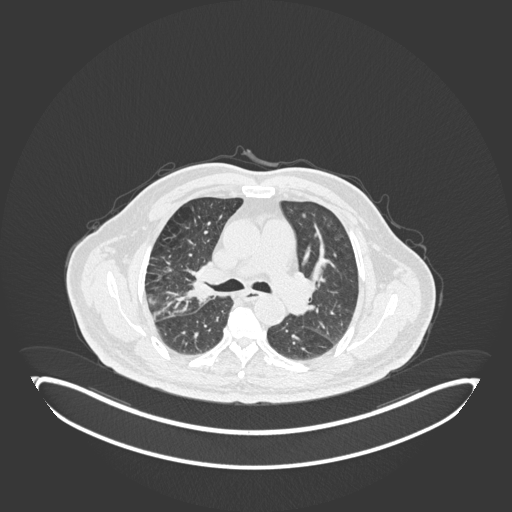
Chest CT, one axial slice. Slice 109 of 247 in the series (ordered by position). 120 kVp. Lung window (W 1500 / L -600 HU). 1 mm slice thickness. 512 × 512 image matrix, field of view 500 × 500 mm. Male patient, age 72 years. Case-level facts recorded for this patient, not image findings: clinical TNM (as recorded): T1c N0 M0; histopathological grade: G2.
Annotated regions visible in this slice (bounding box drawn by a radiologist):
- lung tumour (recorded histology: squamous cell carcinoma): bounding box <177,264,211,307> (left, top, right, bottom; pixels)